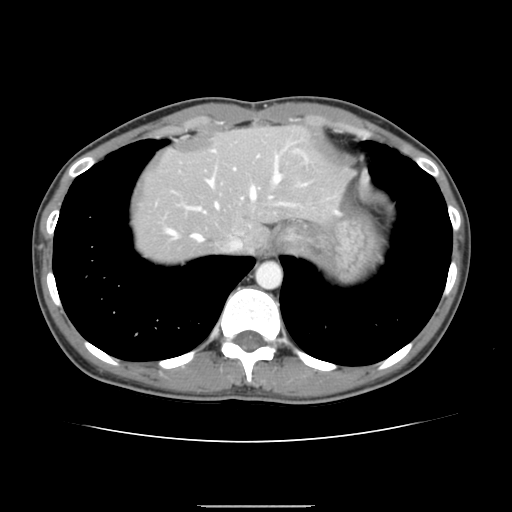
Contrast-enhanced abdominal CT, one axial slice; position 123 of 150 along the scan axis; 120 kVp; intravenous contrast given; soft-tissue window (W 400 / L 40 HU); 2.5 mm slice thickness; 512 × 512 image matrix, field of view 324 × 324 mm. Female patient, age 32 years. From the clinical record (not read from this slice): diagnosis: colorectal cancer liver metastases, imaged before liver resection; multiple liver metastases: yes; largest metastasis: 0.7 cm; disease in both lobes: no.
Outlined on this slice (expert manual segmentation):
- hepatic veins: bounding box <166,156,281,251> (left, top, right, bottom; pixels)
- liver: <133,127,349,263>
- planned liver remnant (the part of the liver to remain after resection): <133,127,349,255>
- portal vein (with intrahepatic branches): <187,150,306,212>